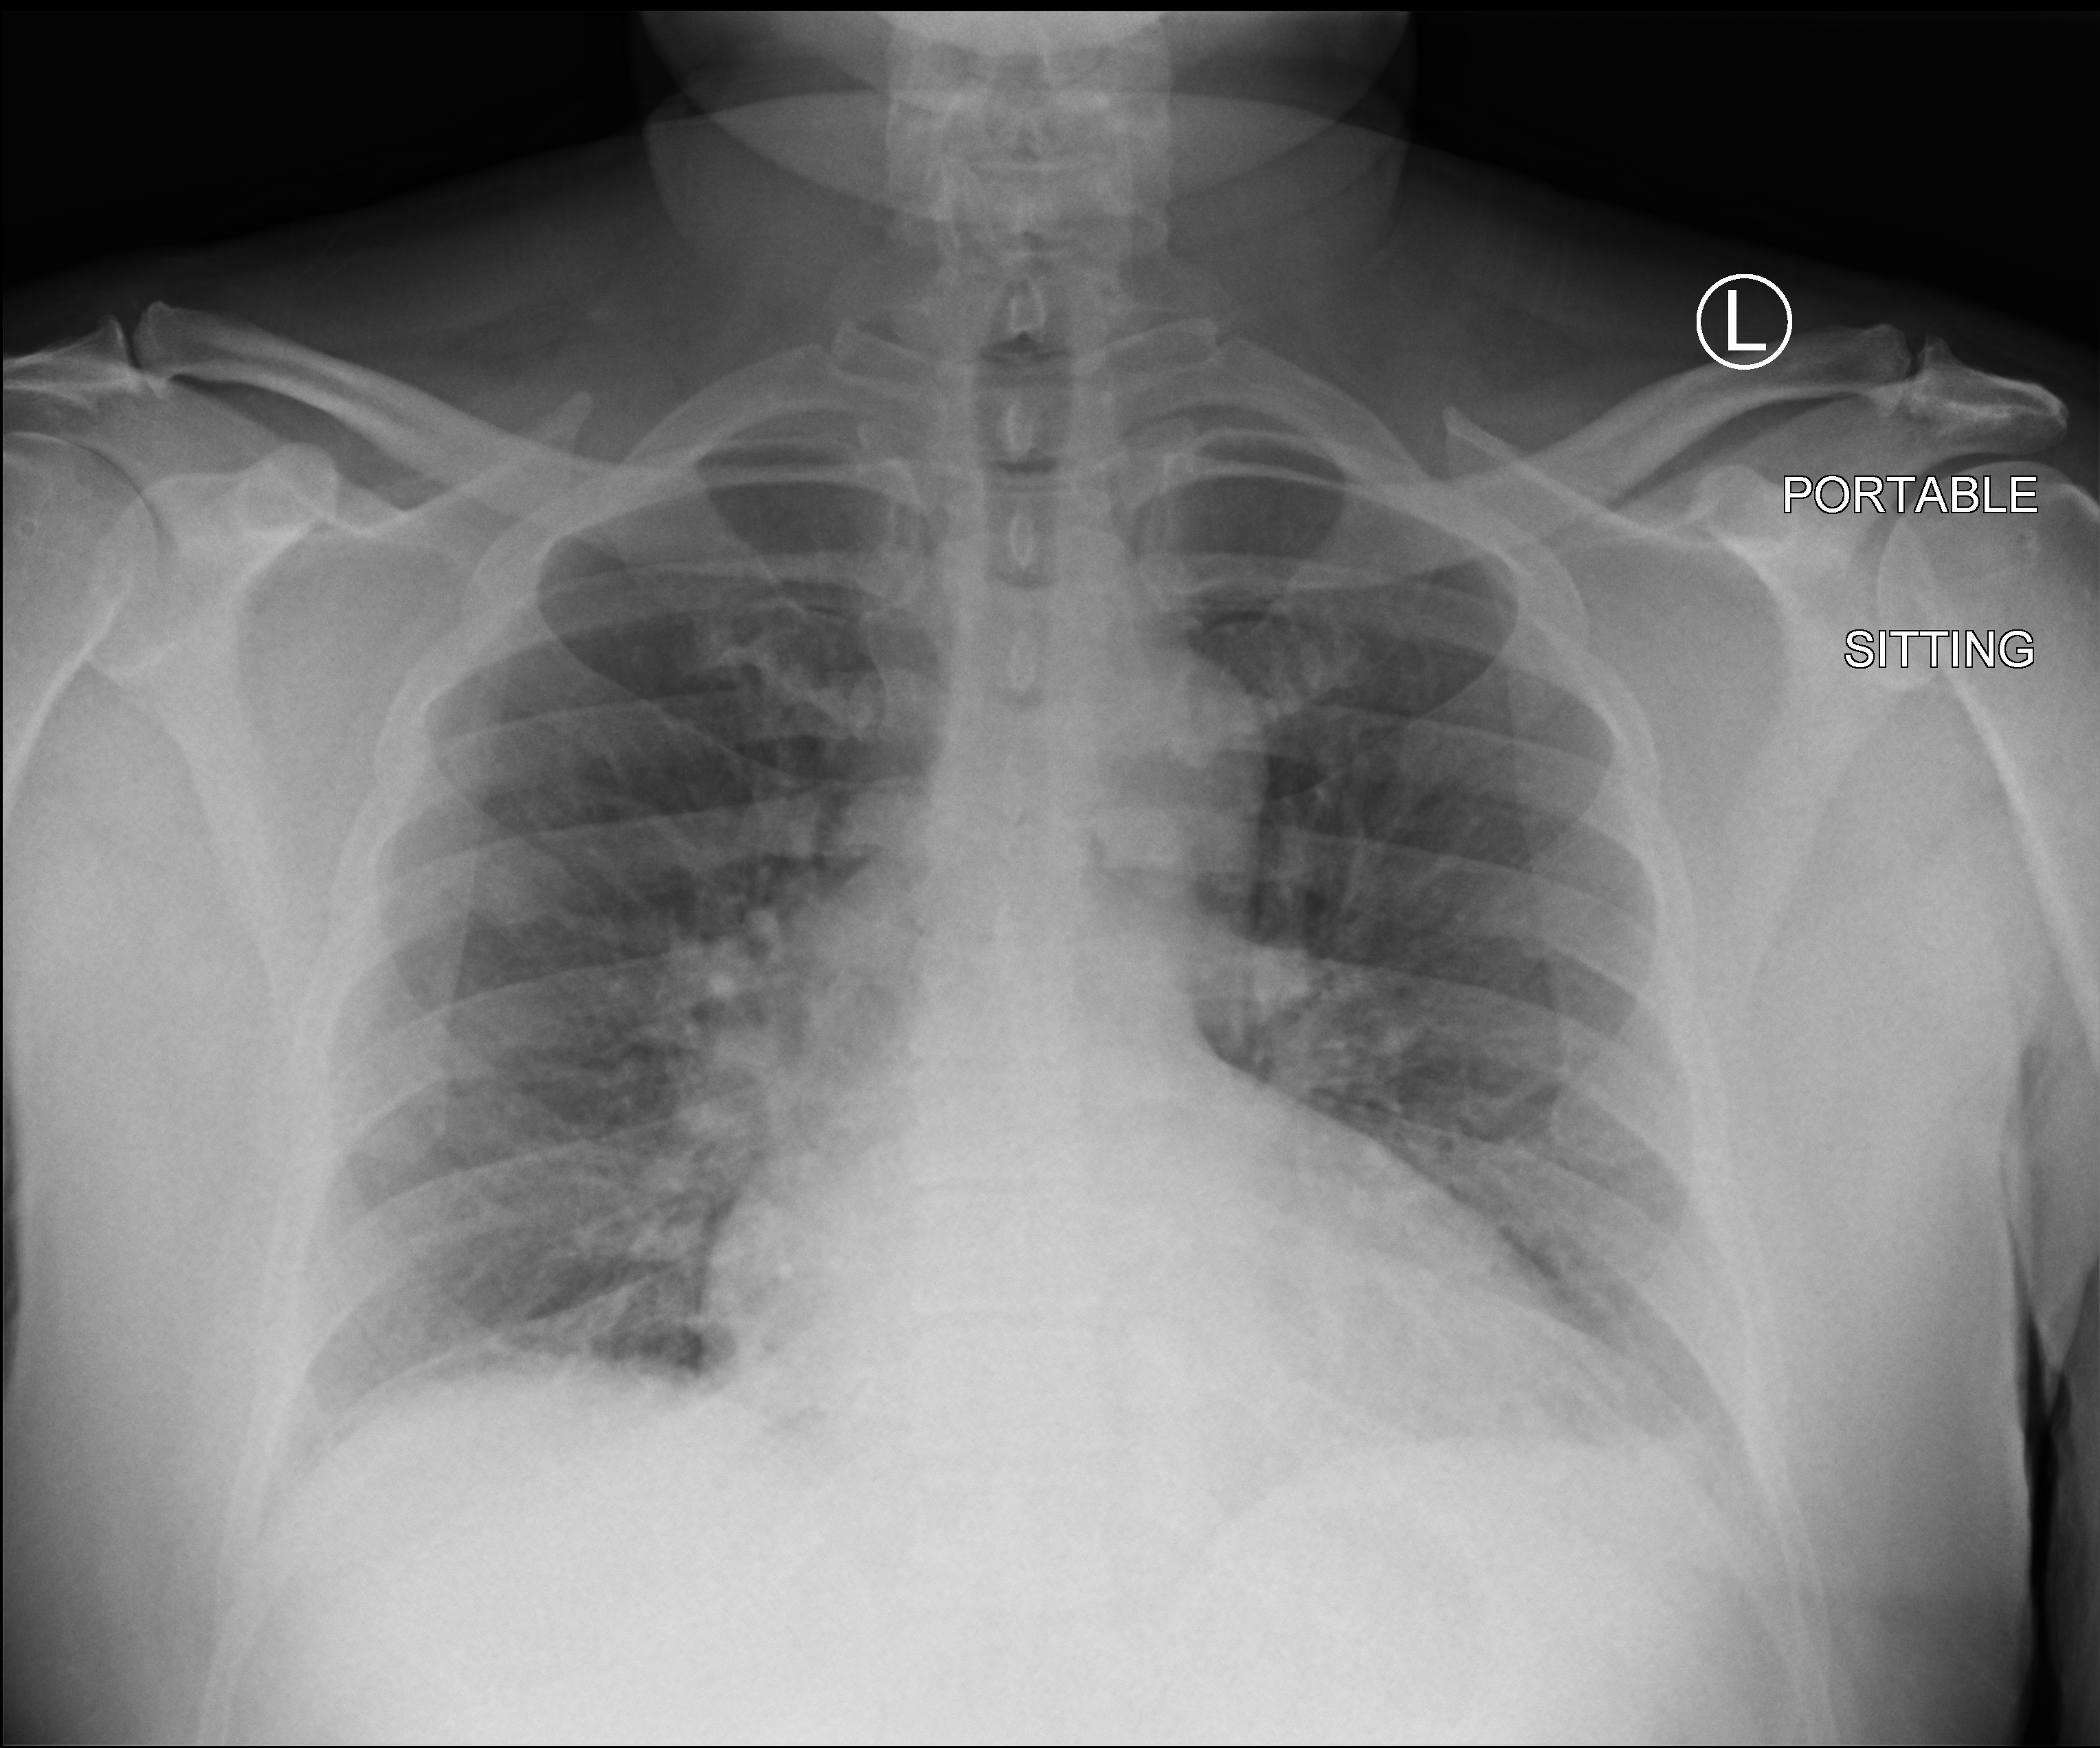
Portable chest radiograph, anteroposterior (AP) projection. Male patient hospitalised with COVID-19, age 18–59 years.
Hospital-stay facts (about this admission, not read from this image; timing relative to this image not recorded): mechanically ventilated during this hospital stay: no; chronic kidney disease (admission record): no; admitted to intensive care during this hospital stay: no.